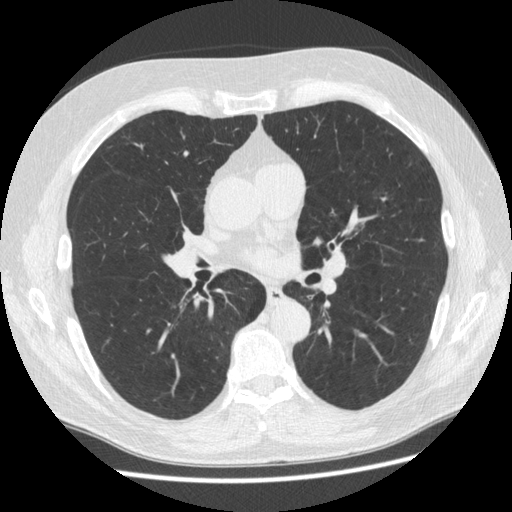
Low-dose screening chest CT, one axial slice; position 296 of 545 along the scan axis; 120 kVp; lung window (W 1500 / L -600 HU); 512 × 512 image matrix, field of view 360 × 360 mm.
Outlined on this slice (outlined manually by an expert reader):
- lesion 1 (nodule, upper lobe of left lung): bounding box (x1, y1, x2, y2) in pixels: (382, 198, 385, 200)